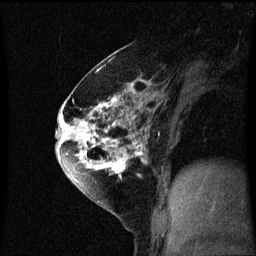
Breast MRI (dynamic contrast-enhanced), one sagittal slice; position 33 of 60 along the scan axis; dynamic contrast-enhanced series, image 2 of 3 at this slice position (ordered by acquisition); 1.5 T; TE 4.2 ms, TR 8.4 ms; 2 mm slice thickness; 256 × 256 image matrix, field of view 200 × 200 mm. Patient: female, 60 years.
Outlined on this slice (semi-automatically segmented with operator editing):
- analysis volume of interest (the breast-tissue region the enhancement analysis was run in; not a lesion): box from (x=64, y=70) to (x=147, y=195) px
- tumour enhancement mask (voxels above the 70 % enhancement threshold inside the analysis volume of interest): (x=64, y=70)–(x=147, y=189)